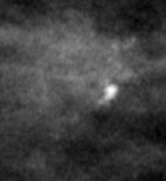
Cropped region of a digitized screen-film mammogram centred on a radiologist-marked abnormality, left breast, CC view, BI-RADS breast density category 2 (scale 1–4).
Marked abnormality: calcifications, morphology pleomorphic, distribution linear; BI-RADS assessment category 4; pathology result (as recorded, not read from the image): malignant.